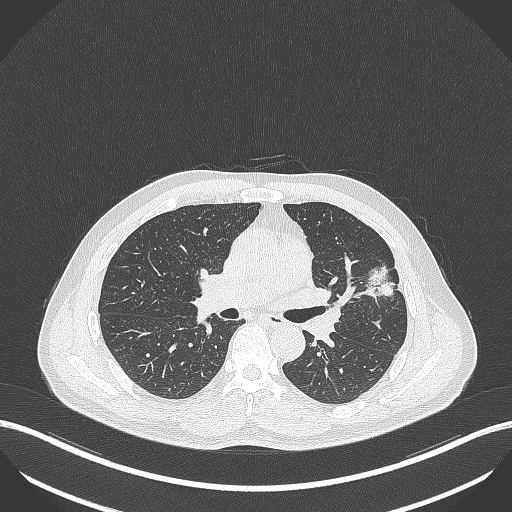
Chest CT, one axial slice. Position 228 of 418 along the scan axis. Reconstruction kernel B70f. 120 kVp. Lung window (W 1500 / L -600 HU). 1 mm slice thickness. 512 × 512 image matrix, field of view 400 × 400 mm. Male patient, age 55 years. From the clinical record (not read from this slice): clinical TNM (as recorded): T1c N0 M0; histopathological grade: G2-3.
Structures marked on this image (rectangle marked by the reading radiologist):
- lung tumour (recorded histology: adenocarcinoma): bounding box (x1, y1, x2, y2) in pixels: (362, 262, 396, 299)